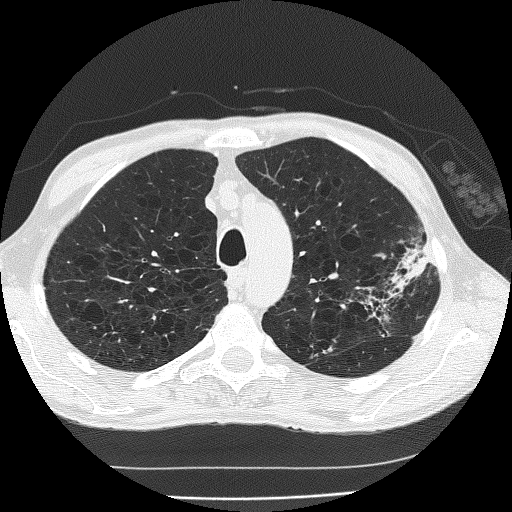
Low-dose screening chest CT, one axial slice; 120 kVp; lung window (W 1500 / L -600 HU); 2 mm slice thickness; 512 × 512 image matrix.
Annotated regions visible in this slice (outlined manually by an expert reader):
- lesion 1 (tumor, upper lobe of left lung): box from (x=388, y=246) to (x=428, y=297) px